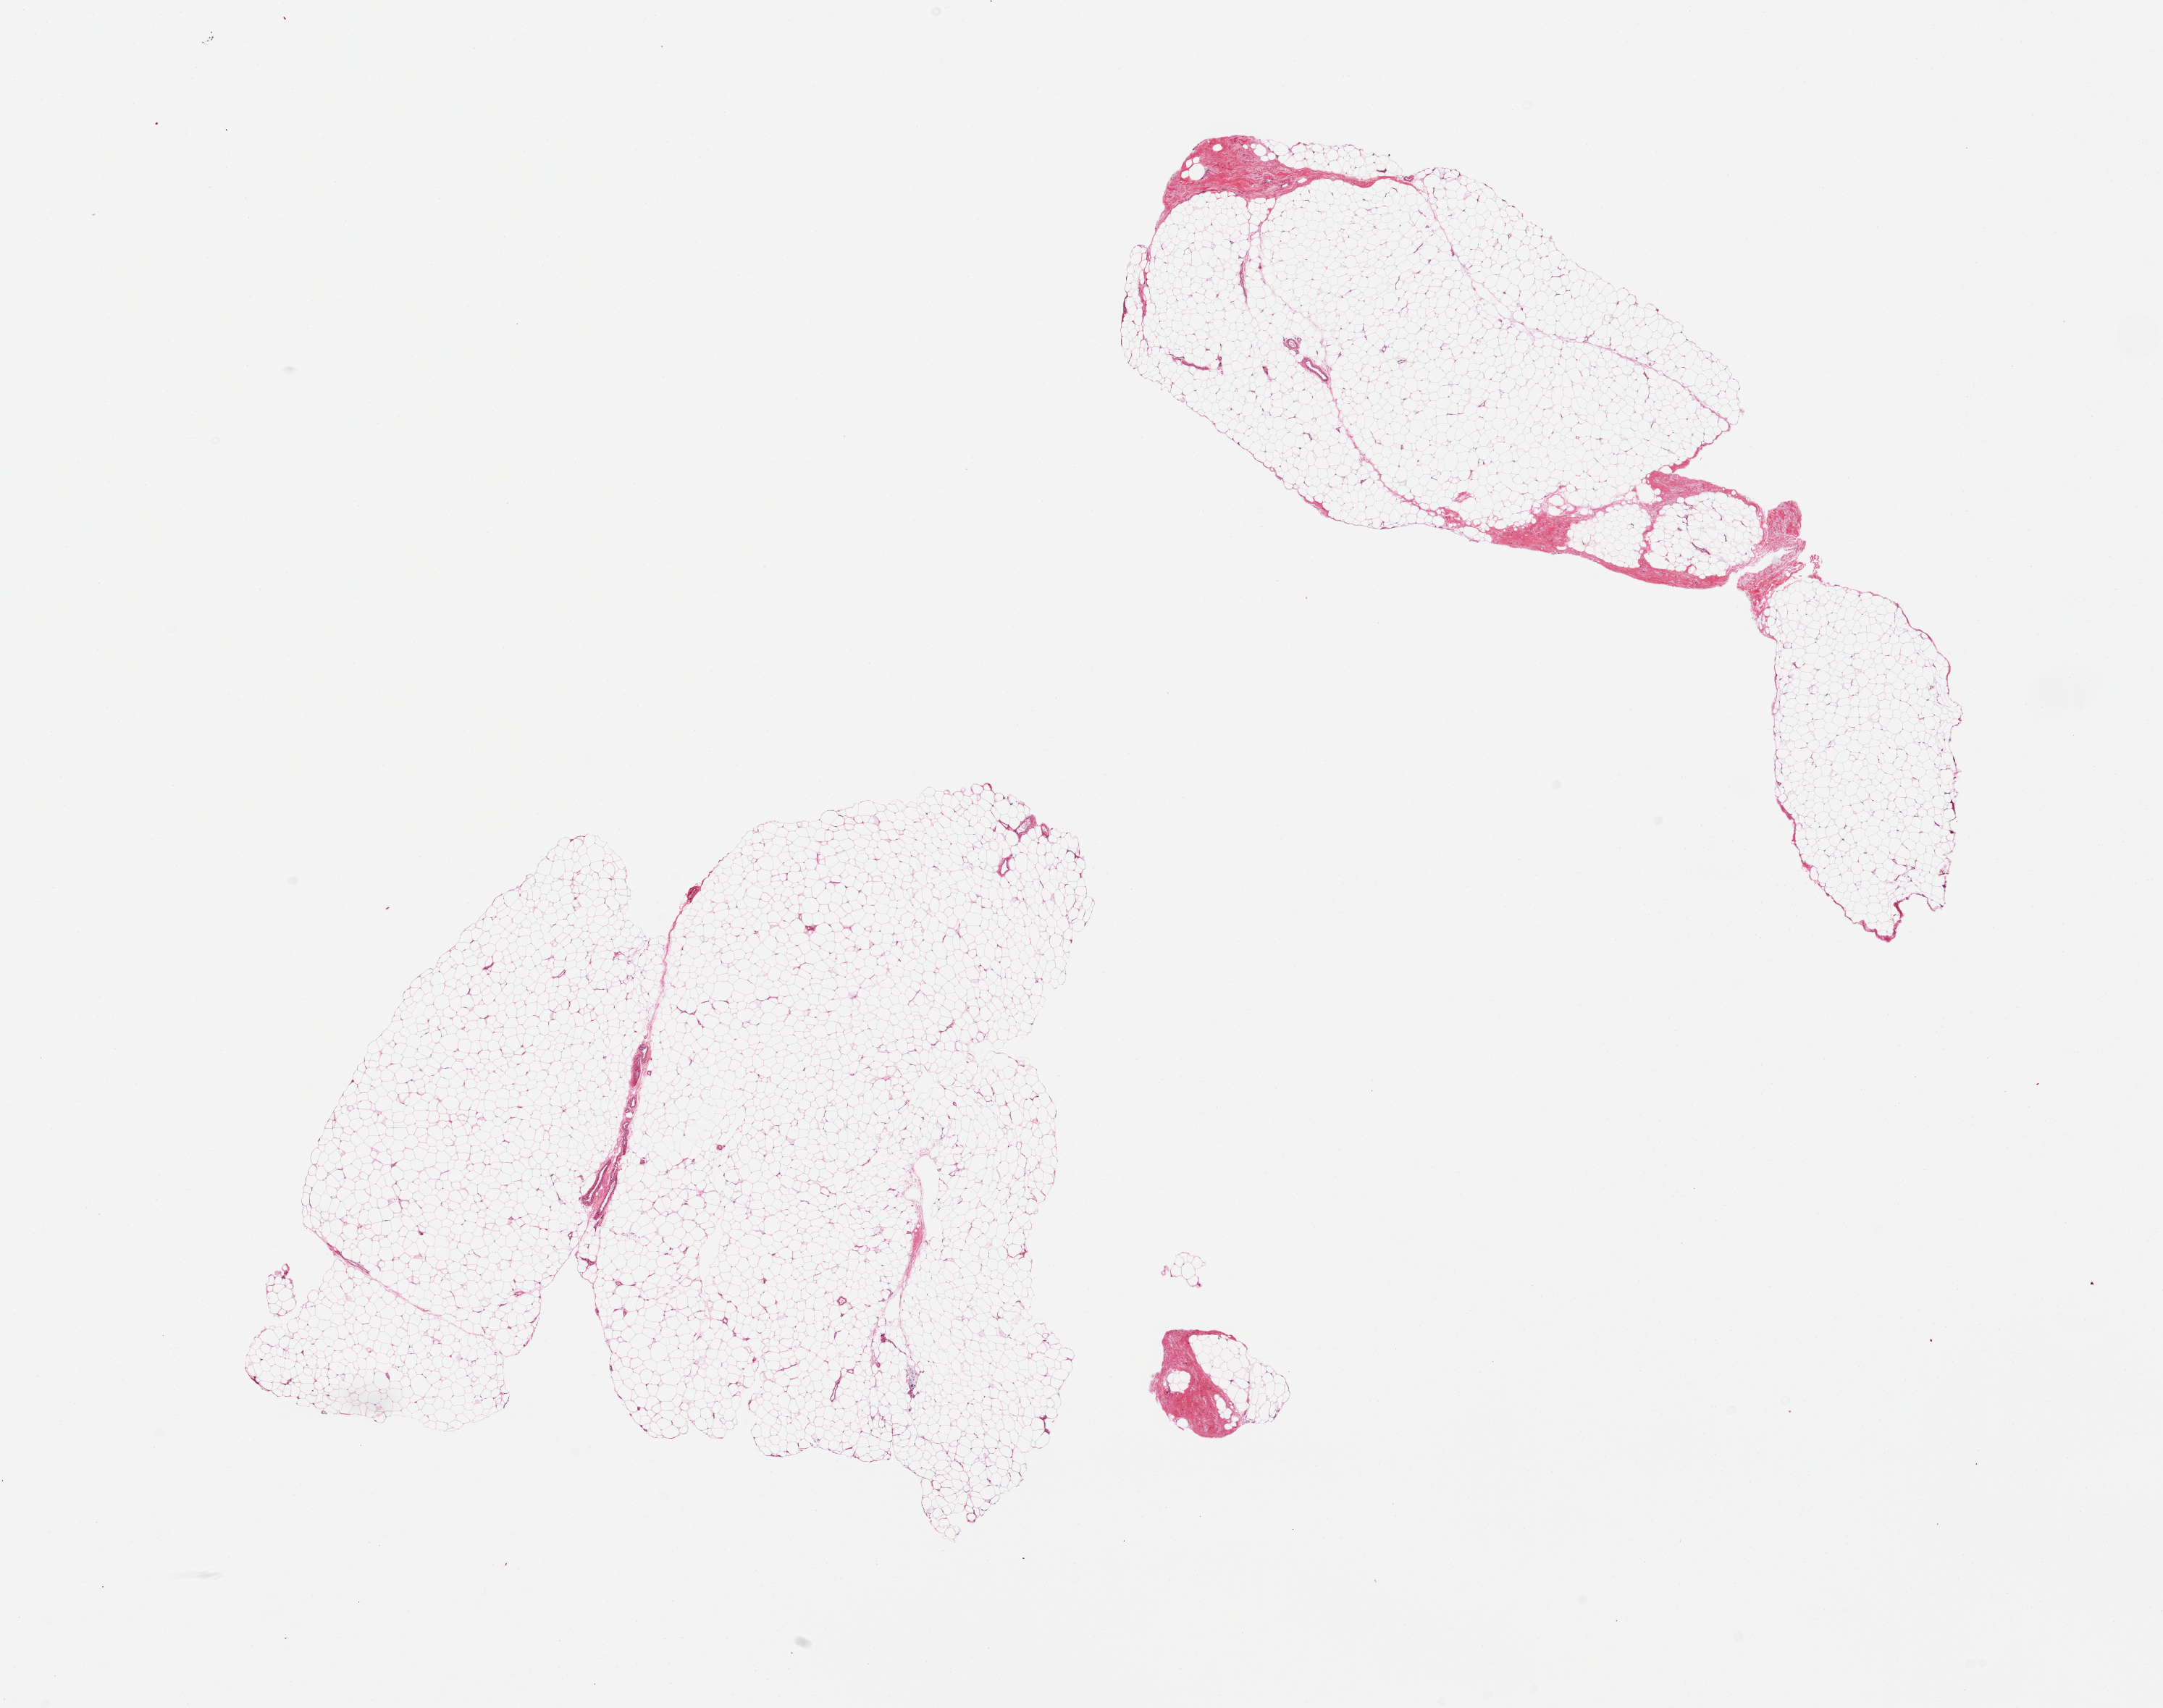
Haematoxylin and eosin whole-slide image, a low-resolution overview of the entire scanned area, about 23.6 x 18.7 mm (slide scanned at 20x). PAXgene-fixed, paraffin-embedded tissue. Section of adipose tissue (target tissue). Tissue donor sample.
Reviewer comment on this tissue sample: 2 pieces.